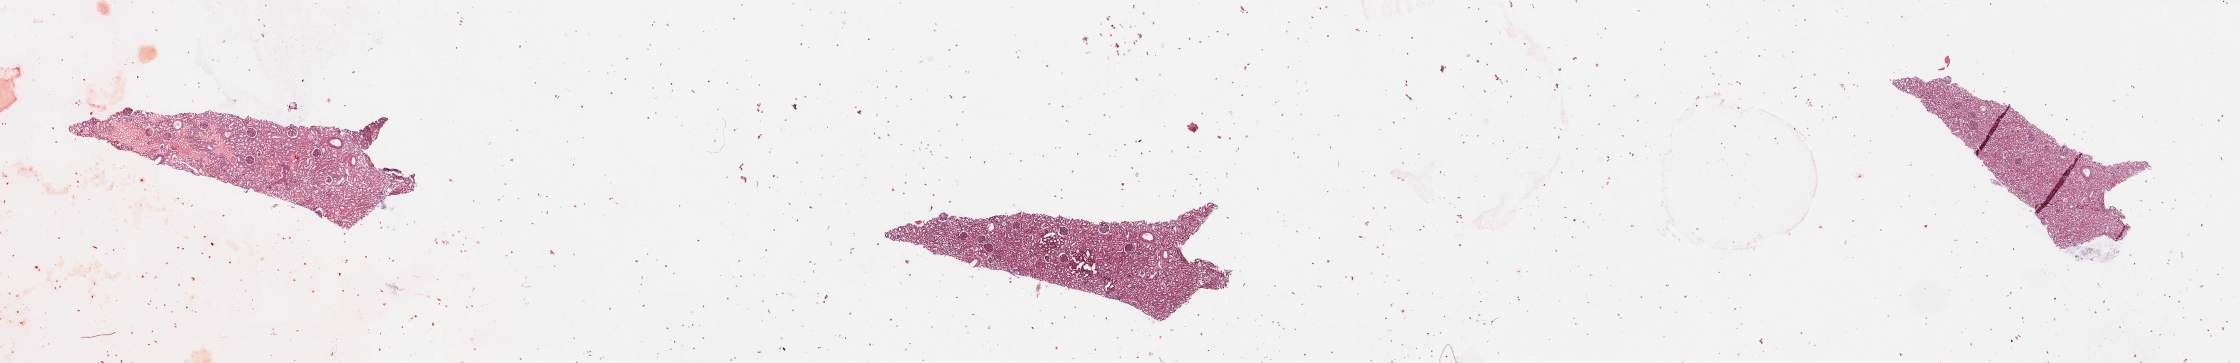
Digitized H&E tissue section (whole slide), shown as a low-resolution overview of the whole scanned area (about 35.4 x 5.7 mm, acquisition: 20x scan); normal (non-tumour) tissue sample, sampled site: kidney. Male, 48 y/o.
This section: normal (non-tumour) tissue from the same patient. Patient diagnosis: Renal cell carcinoma, NOS.